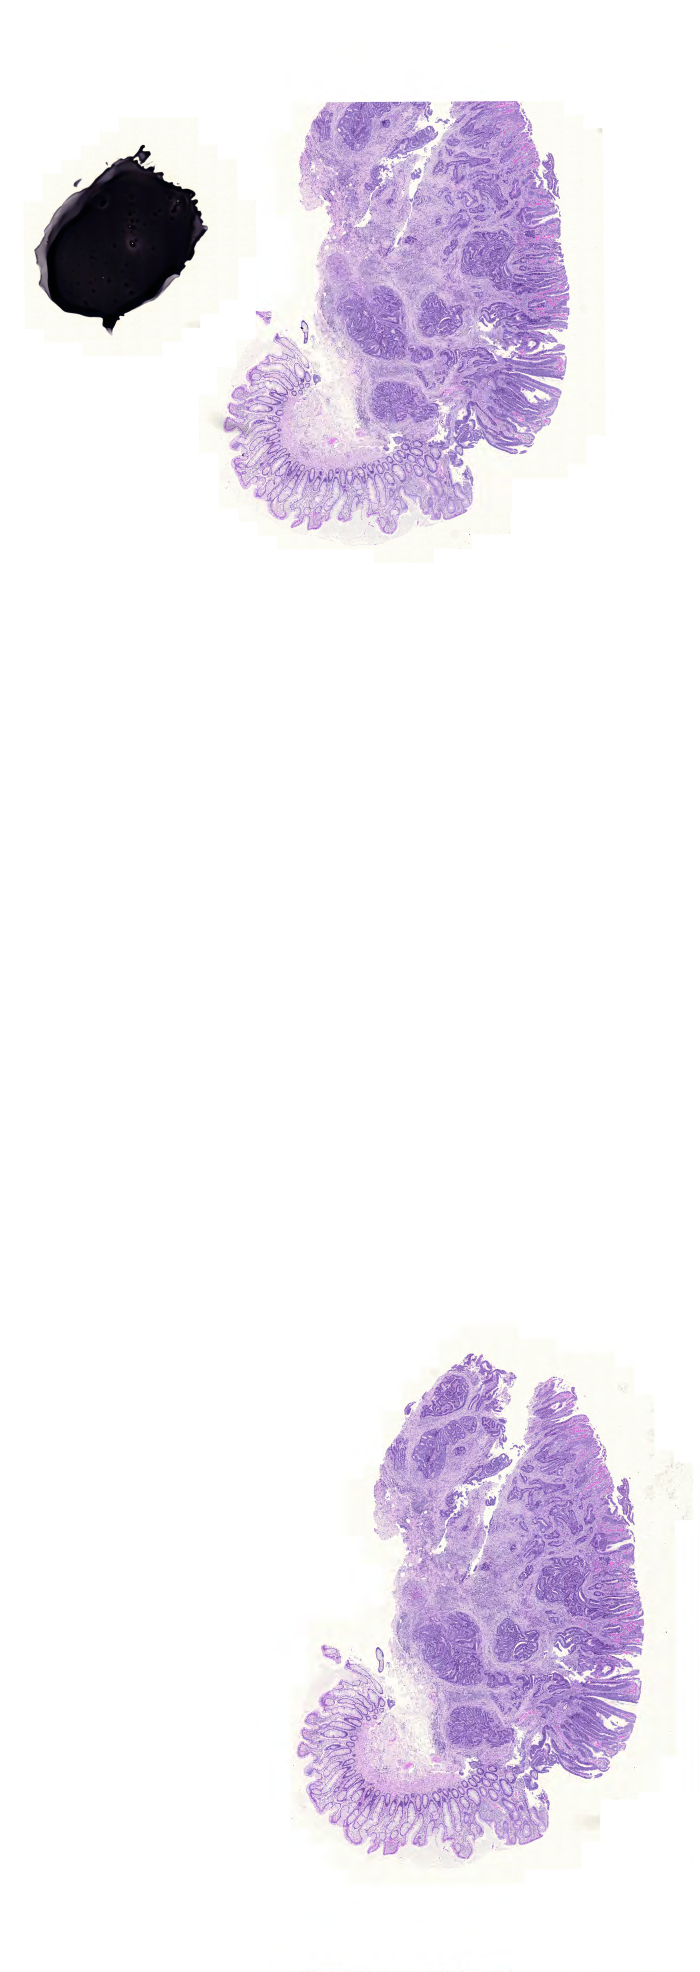
Whole-slide histology image, Hematoxylin and eosin (H&E) stained — a low-resolution overview of the entire scanned area, about 10.4 x 29.3 mm (acquisition: 20x scan); formalin-fixed paraffin-embedded (FFPE) diagnostic section; colon, primary tumour sample. Male patient; age at initial diagnosis 68 years.
- AJCC pathologic stage: I (6th edition)
- diagnosis: Adenocarcinoma, NOS